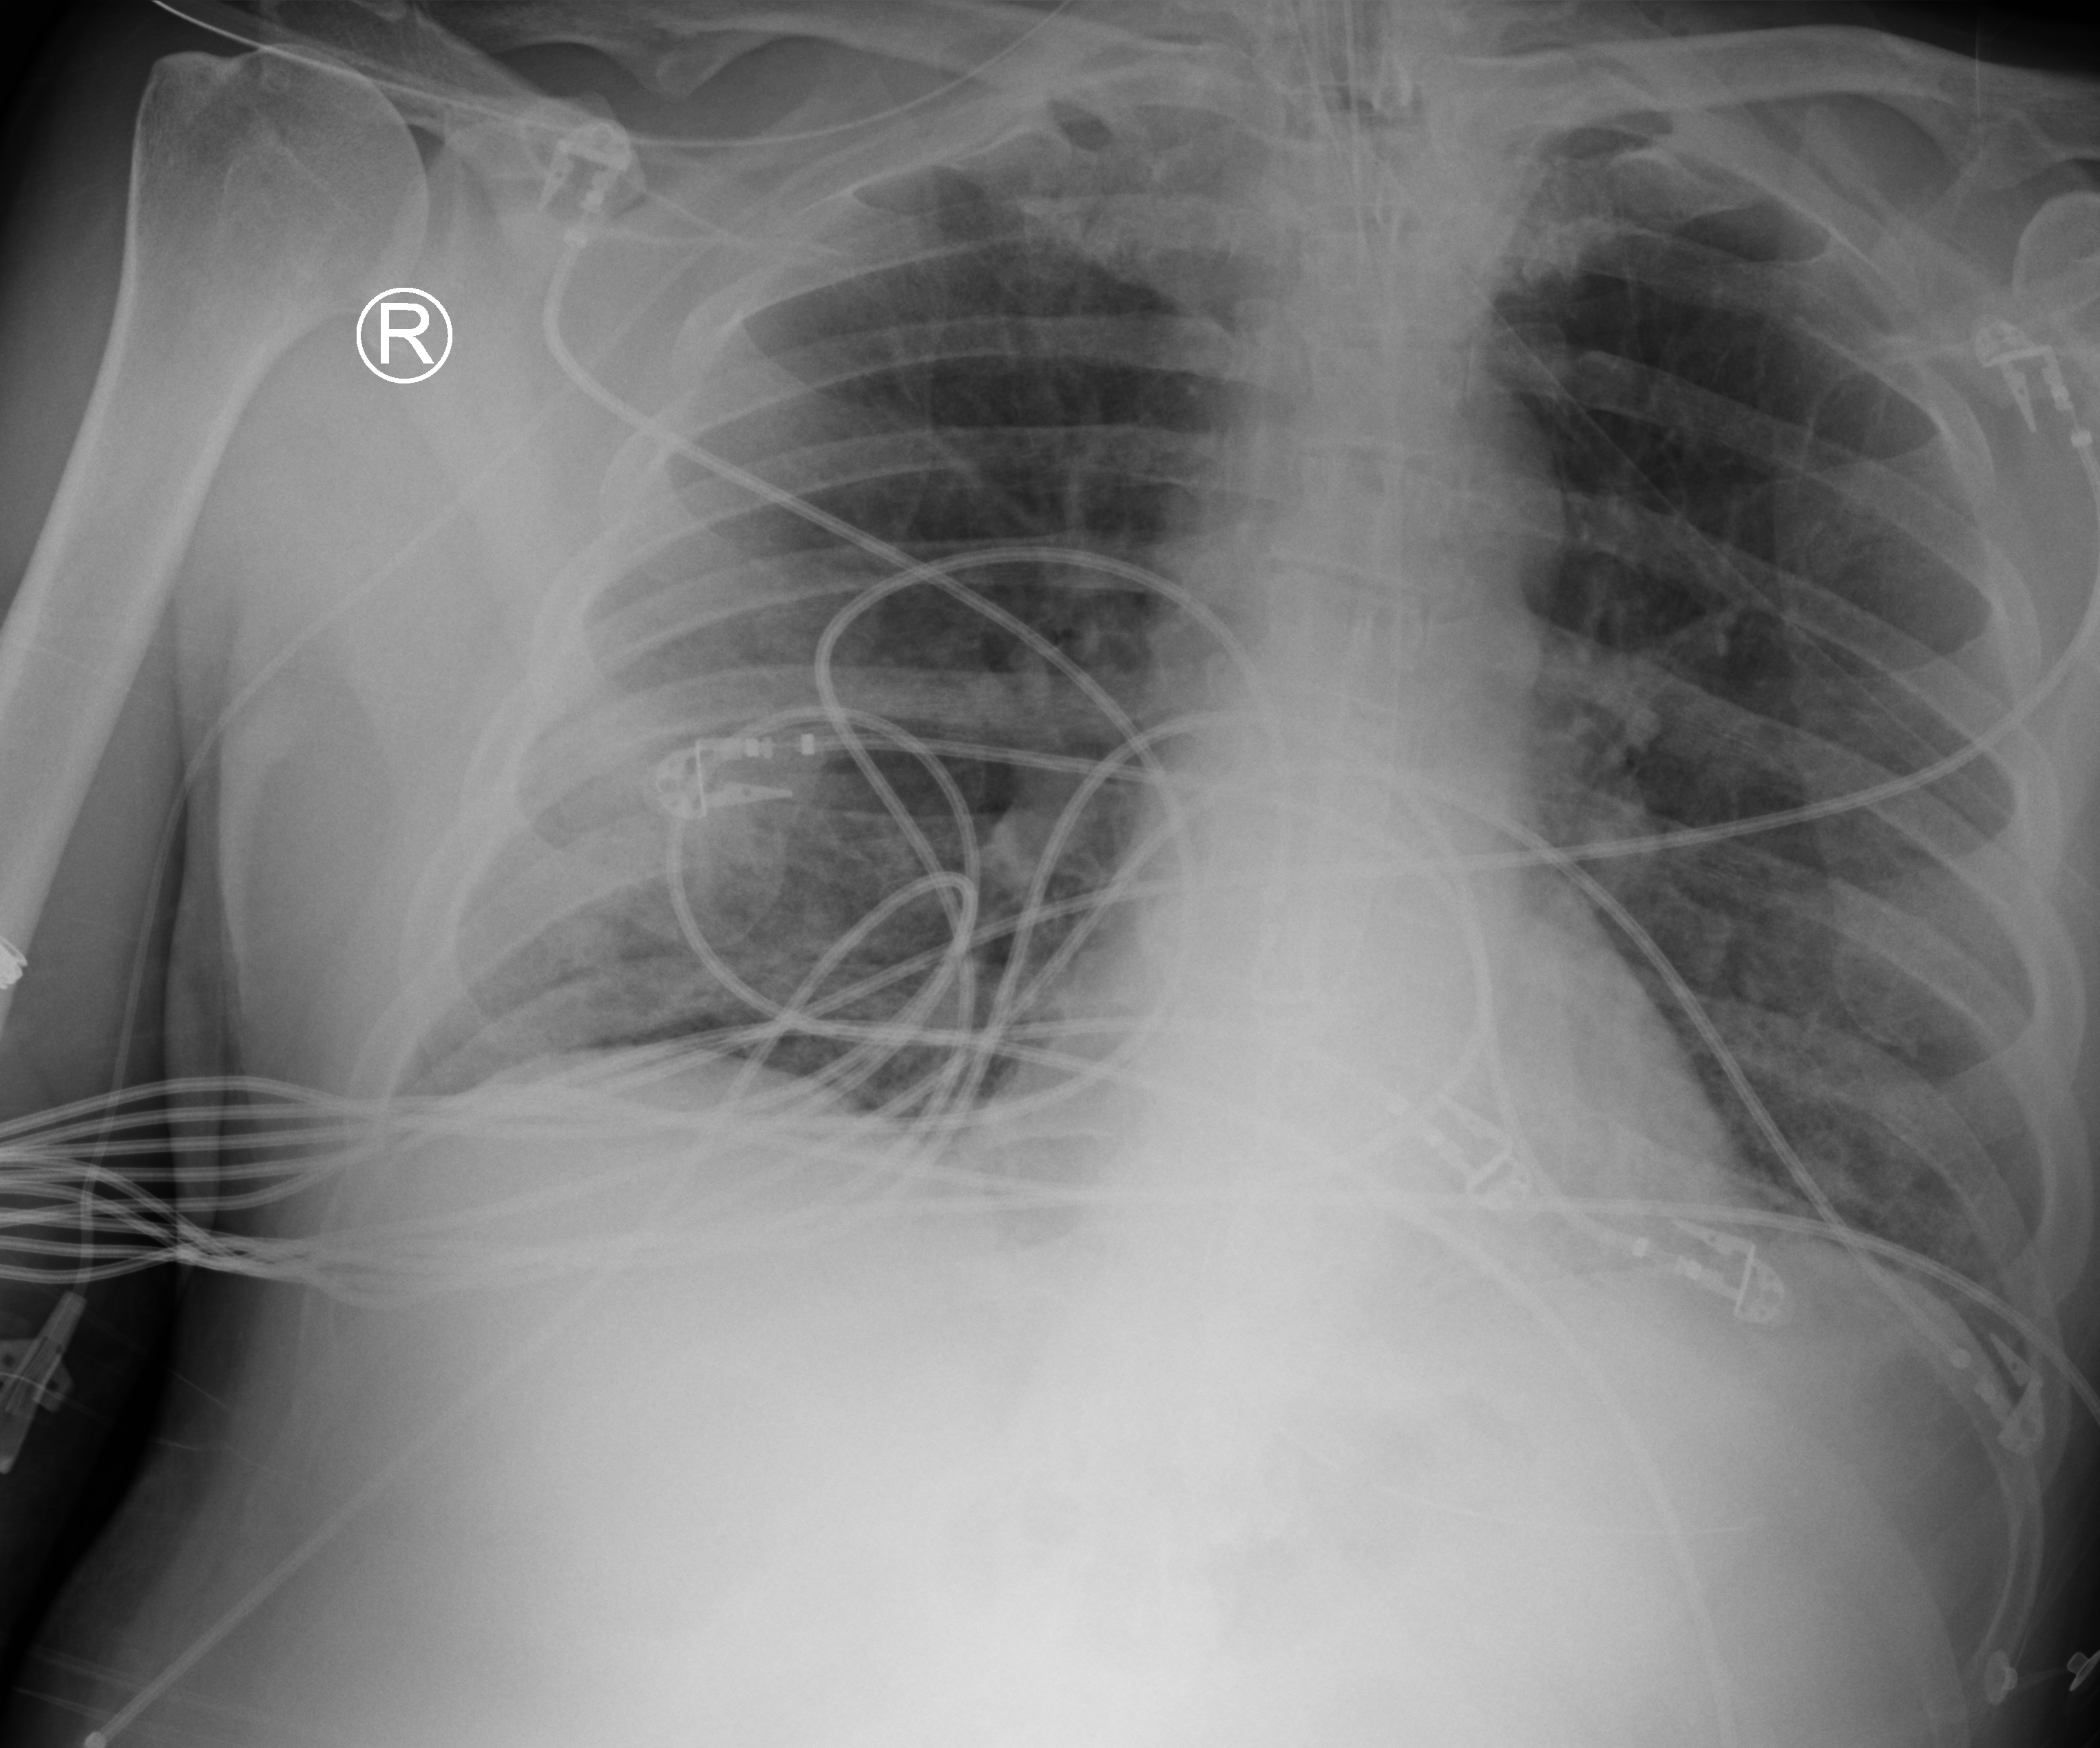
Chest X-ray (portable); anteroposterior (AP) projection. Patient hospitalised with COVID-19; male, aged 60–74 years.
From the hospital-stay record, not from the radiograph (when in the stay this image was taken is not recorded): chronic kidney disease (admission record): no.